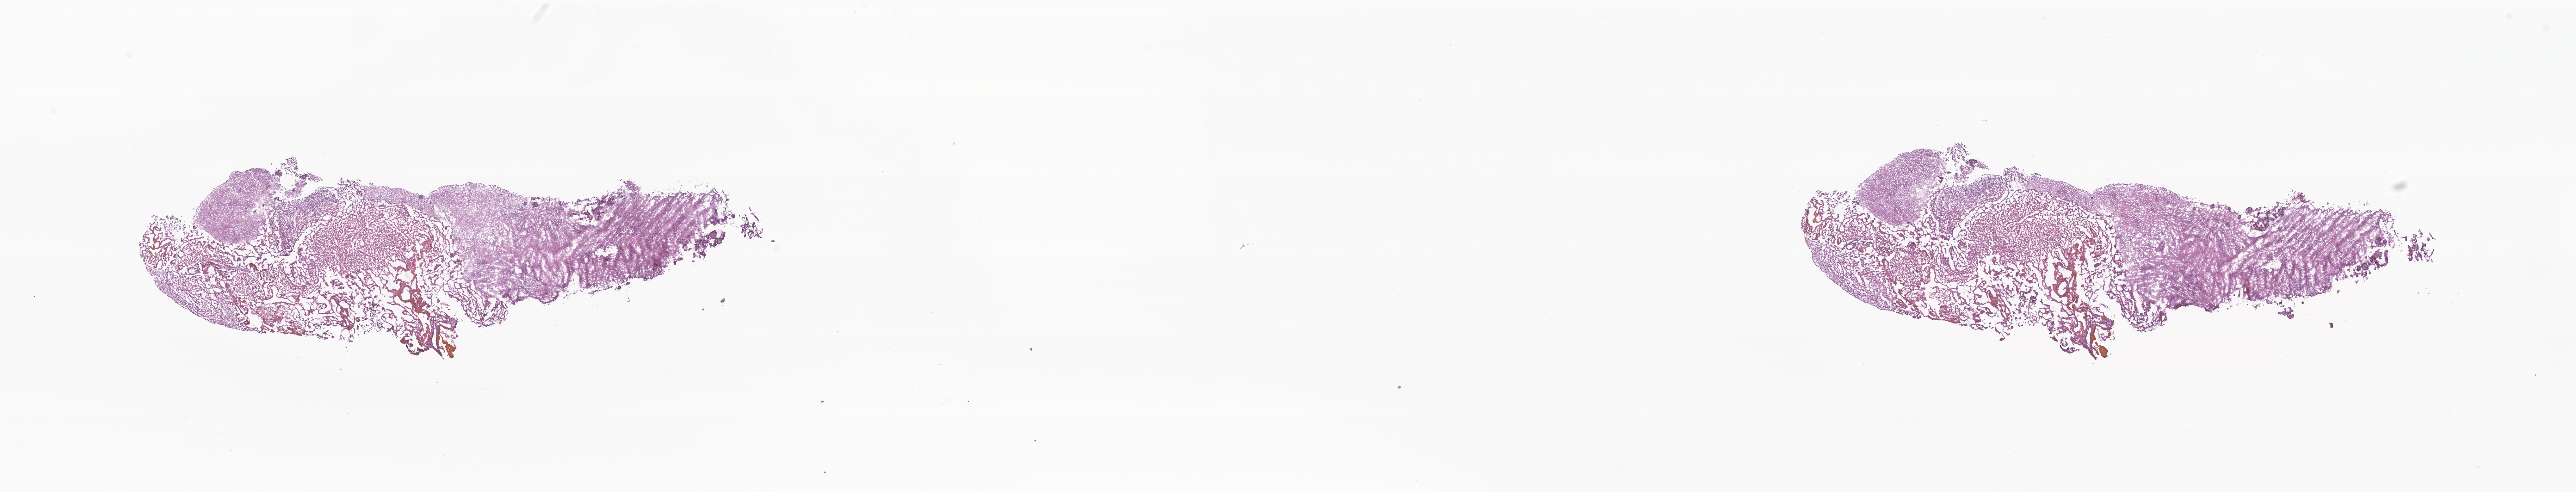
Whole-slide image, haematoxylin and eosin stain of tumor tissue from the brain, shown as a low-resolution overview of the whole scanned area (about 34.3 x 6.6 mm), frozen section. Patient female; age 69 months (5 years 9 months).
Diagnosis (ICD-O-3 morphology term): Glioma, malignant.